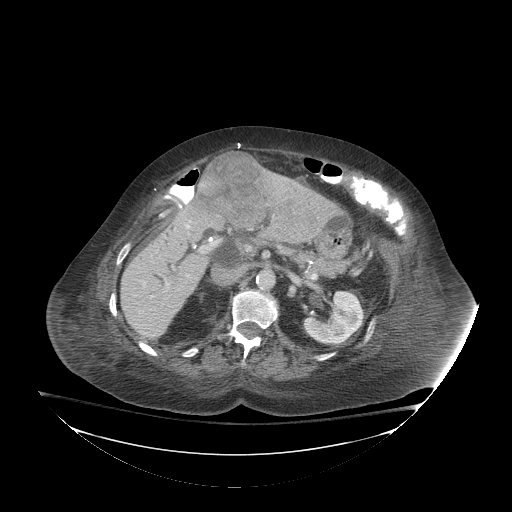
Contrast-enhanced abdominal CT (liver protocol), one axial slice; slice 43 of 81 in the series (ordered by position); 140 kVp; soft-tissue window (W 400 / L 40 HU); 2.5 mm slice thickness; 512 × 512 image matrix, field of view 500 × 500 mm. From the clinical record (not read from this slice): diagnosis: hepatocellular carcinoma (patient treated with transarterial chemoembolisation; whether this scan precedes or follows treatment is not stated here); TNM stage (as recorded): Stage-I; Child-Pugh class: B.
Structures marked on this image (semi-automatically segmented with operator editing):
- liver parenchyma outside the tumour (the mass and vessels are separate outlines, so this box may not span the whole liver): bounding box <120,172,340,339> (left, top, right, bottom; pixels)
- mass: <196,152,271,228>
- liver vessels: <151,224,203,297>